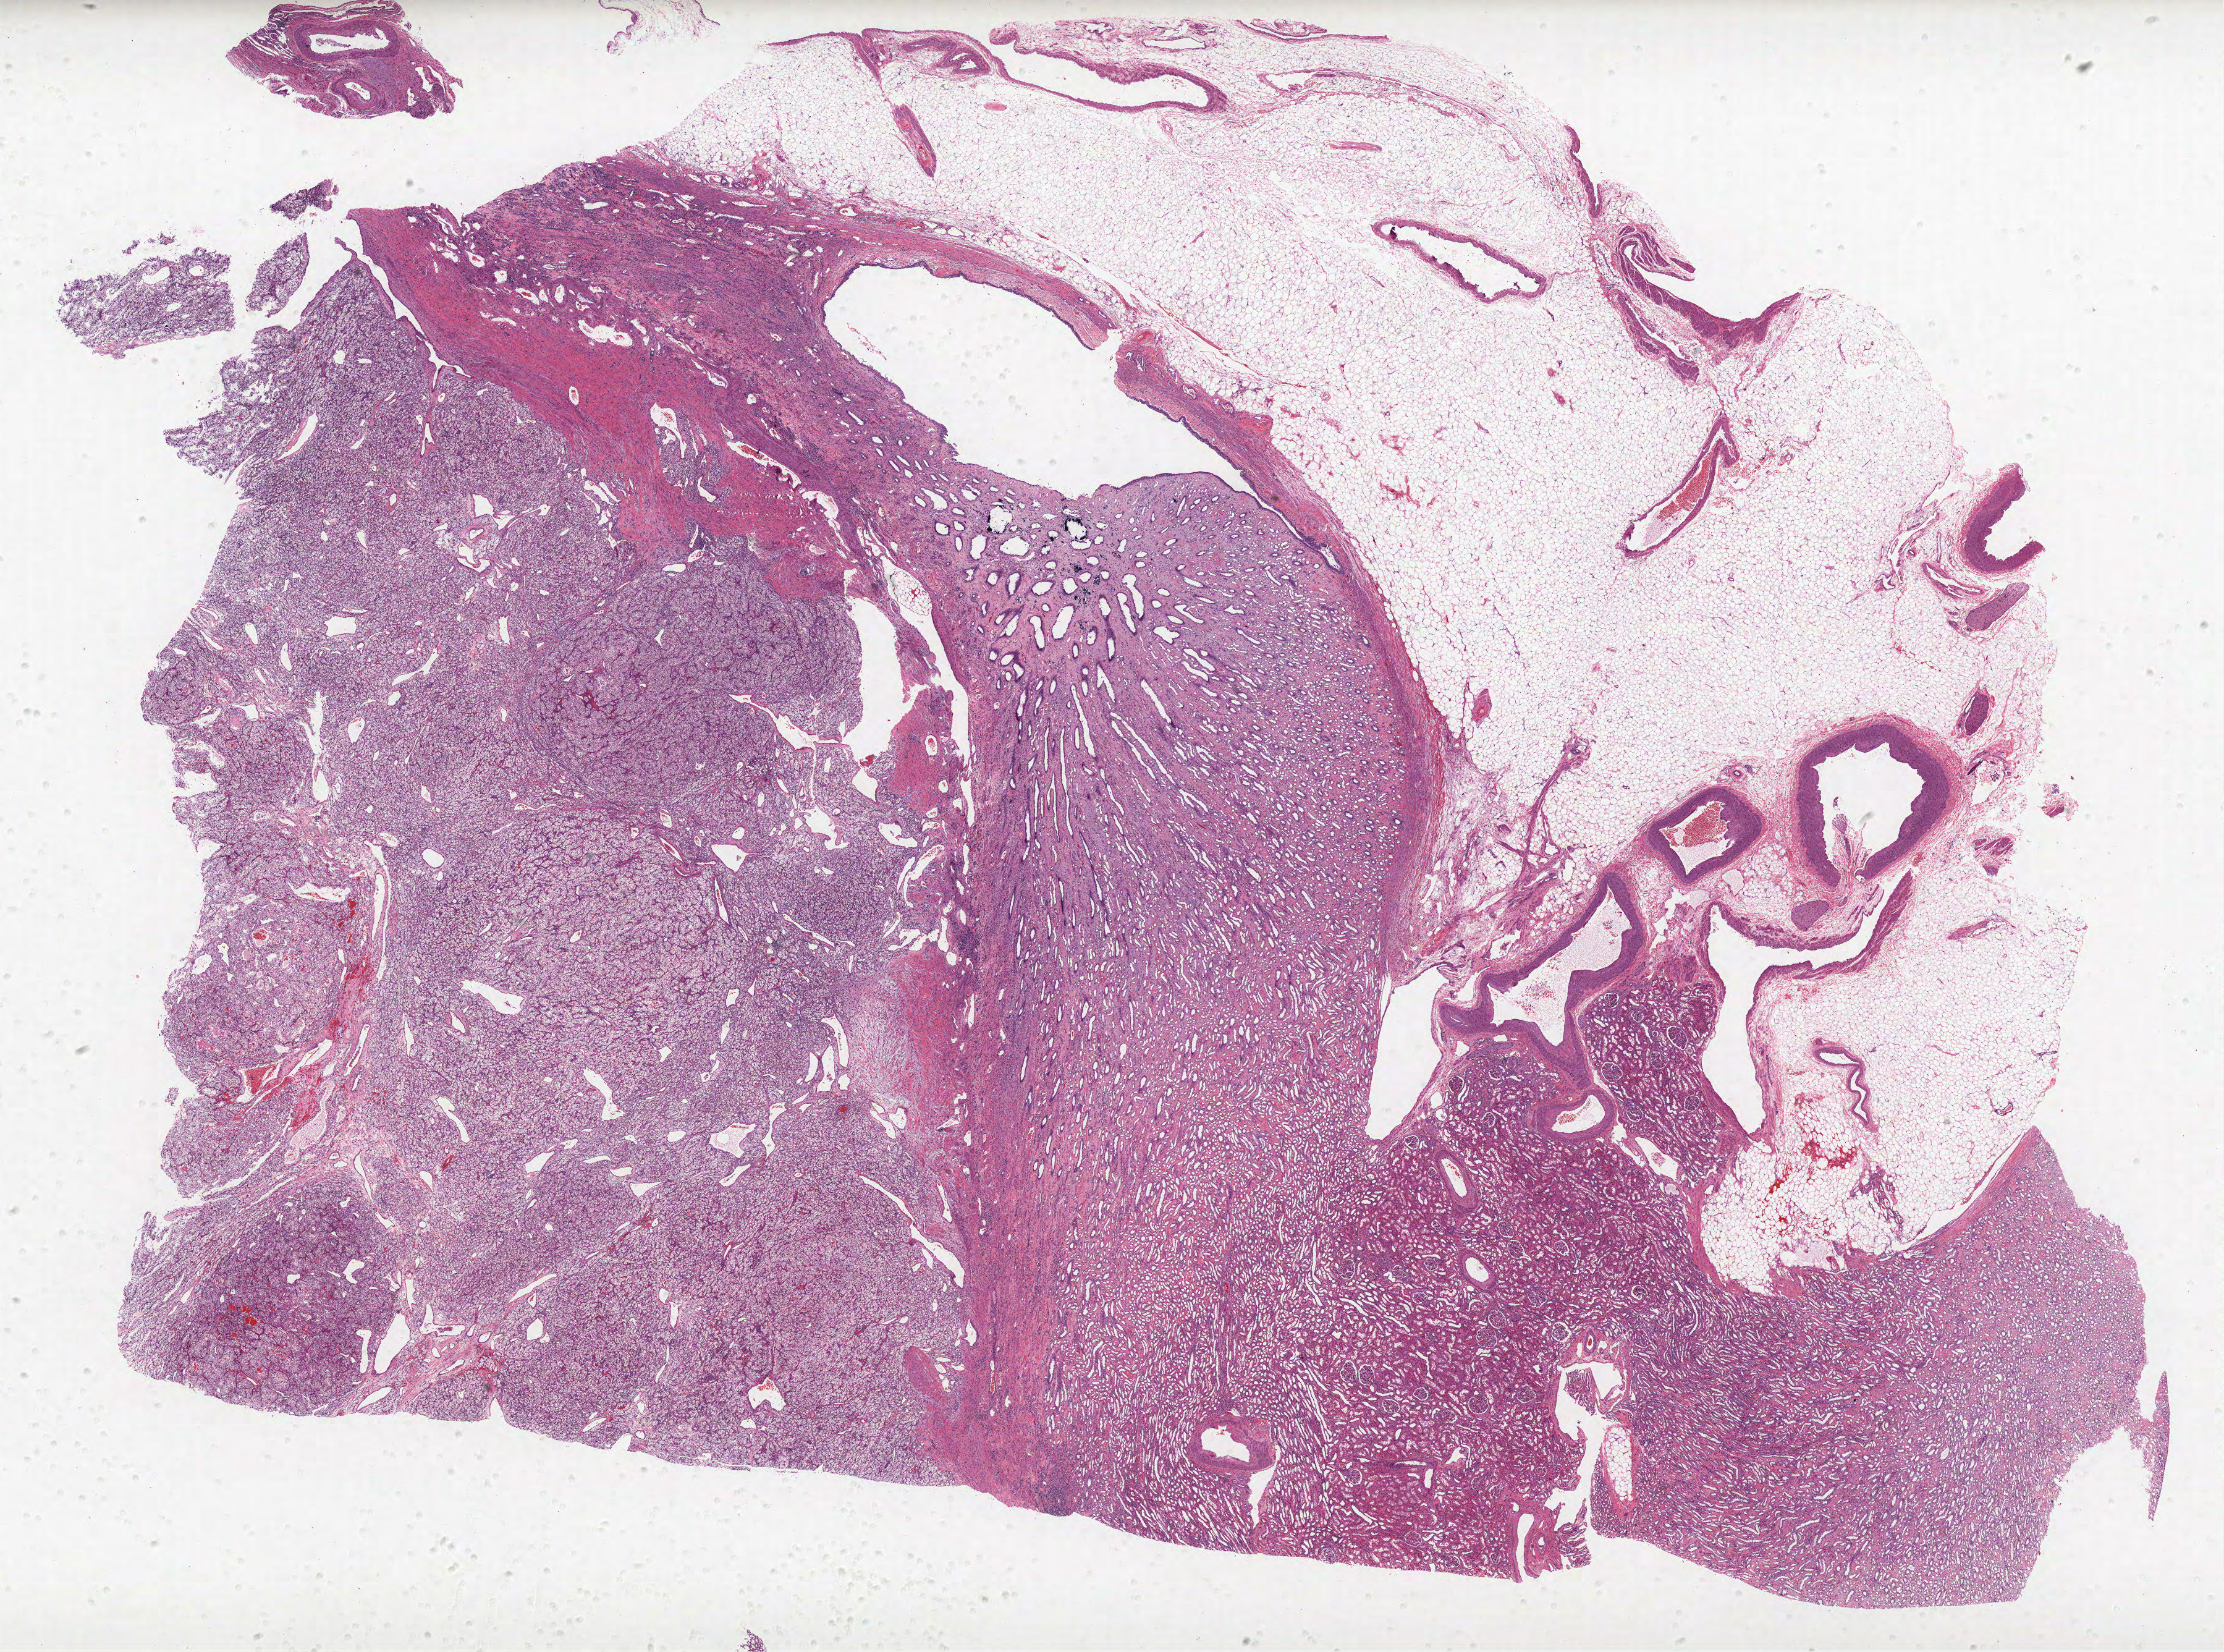
H&E whole-slide image, whole scanned area (about 28.8 x 21.4 mm) shown as a low-resolution overview; formalin-fixed paraffin-embedded (FFPE) diagnostic section; sample: primary tumour, kidney. Patient: male, age at initial diagnosis 63 years. Histologic grade: G3 (poorly differentiated).
- AJCC pathologic stage: I
- pathologic diagnosis: Clear cell adenocarcinoma, NOS